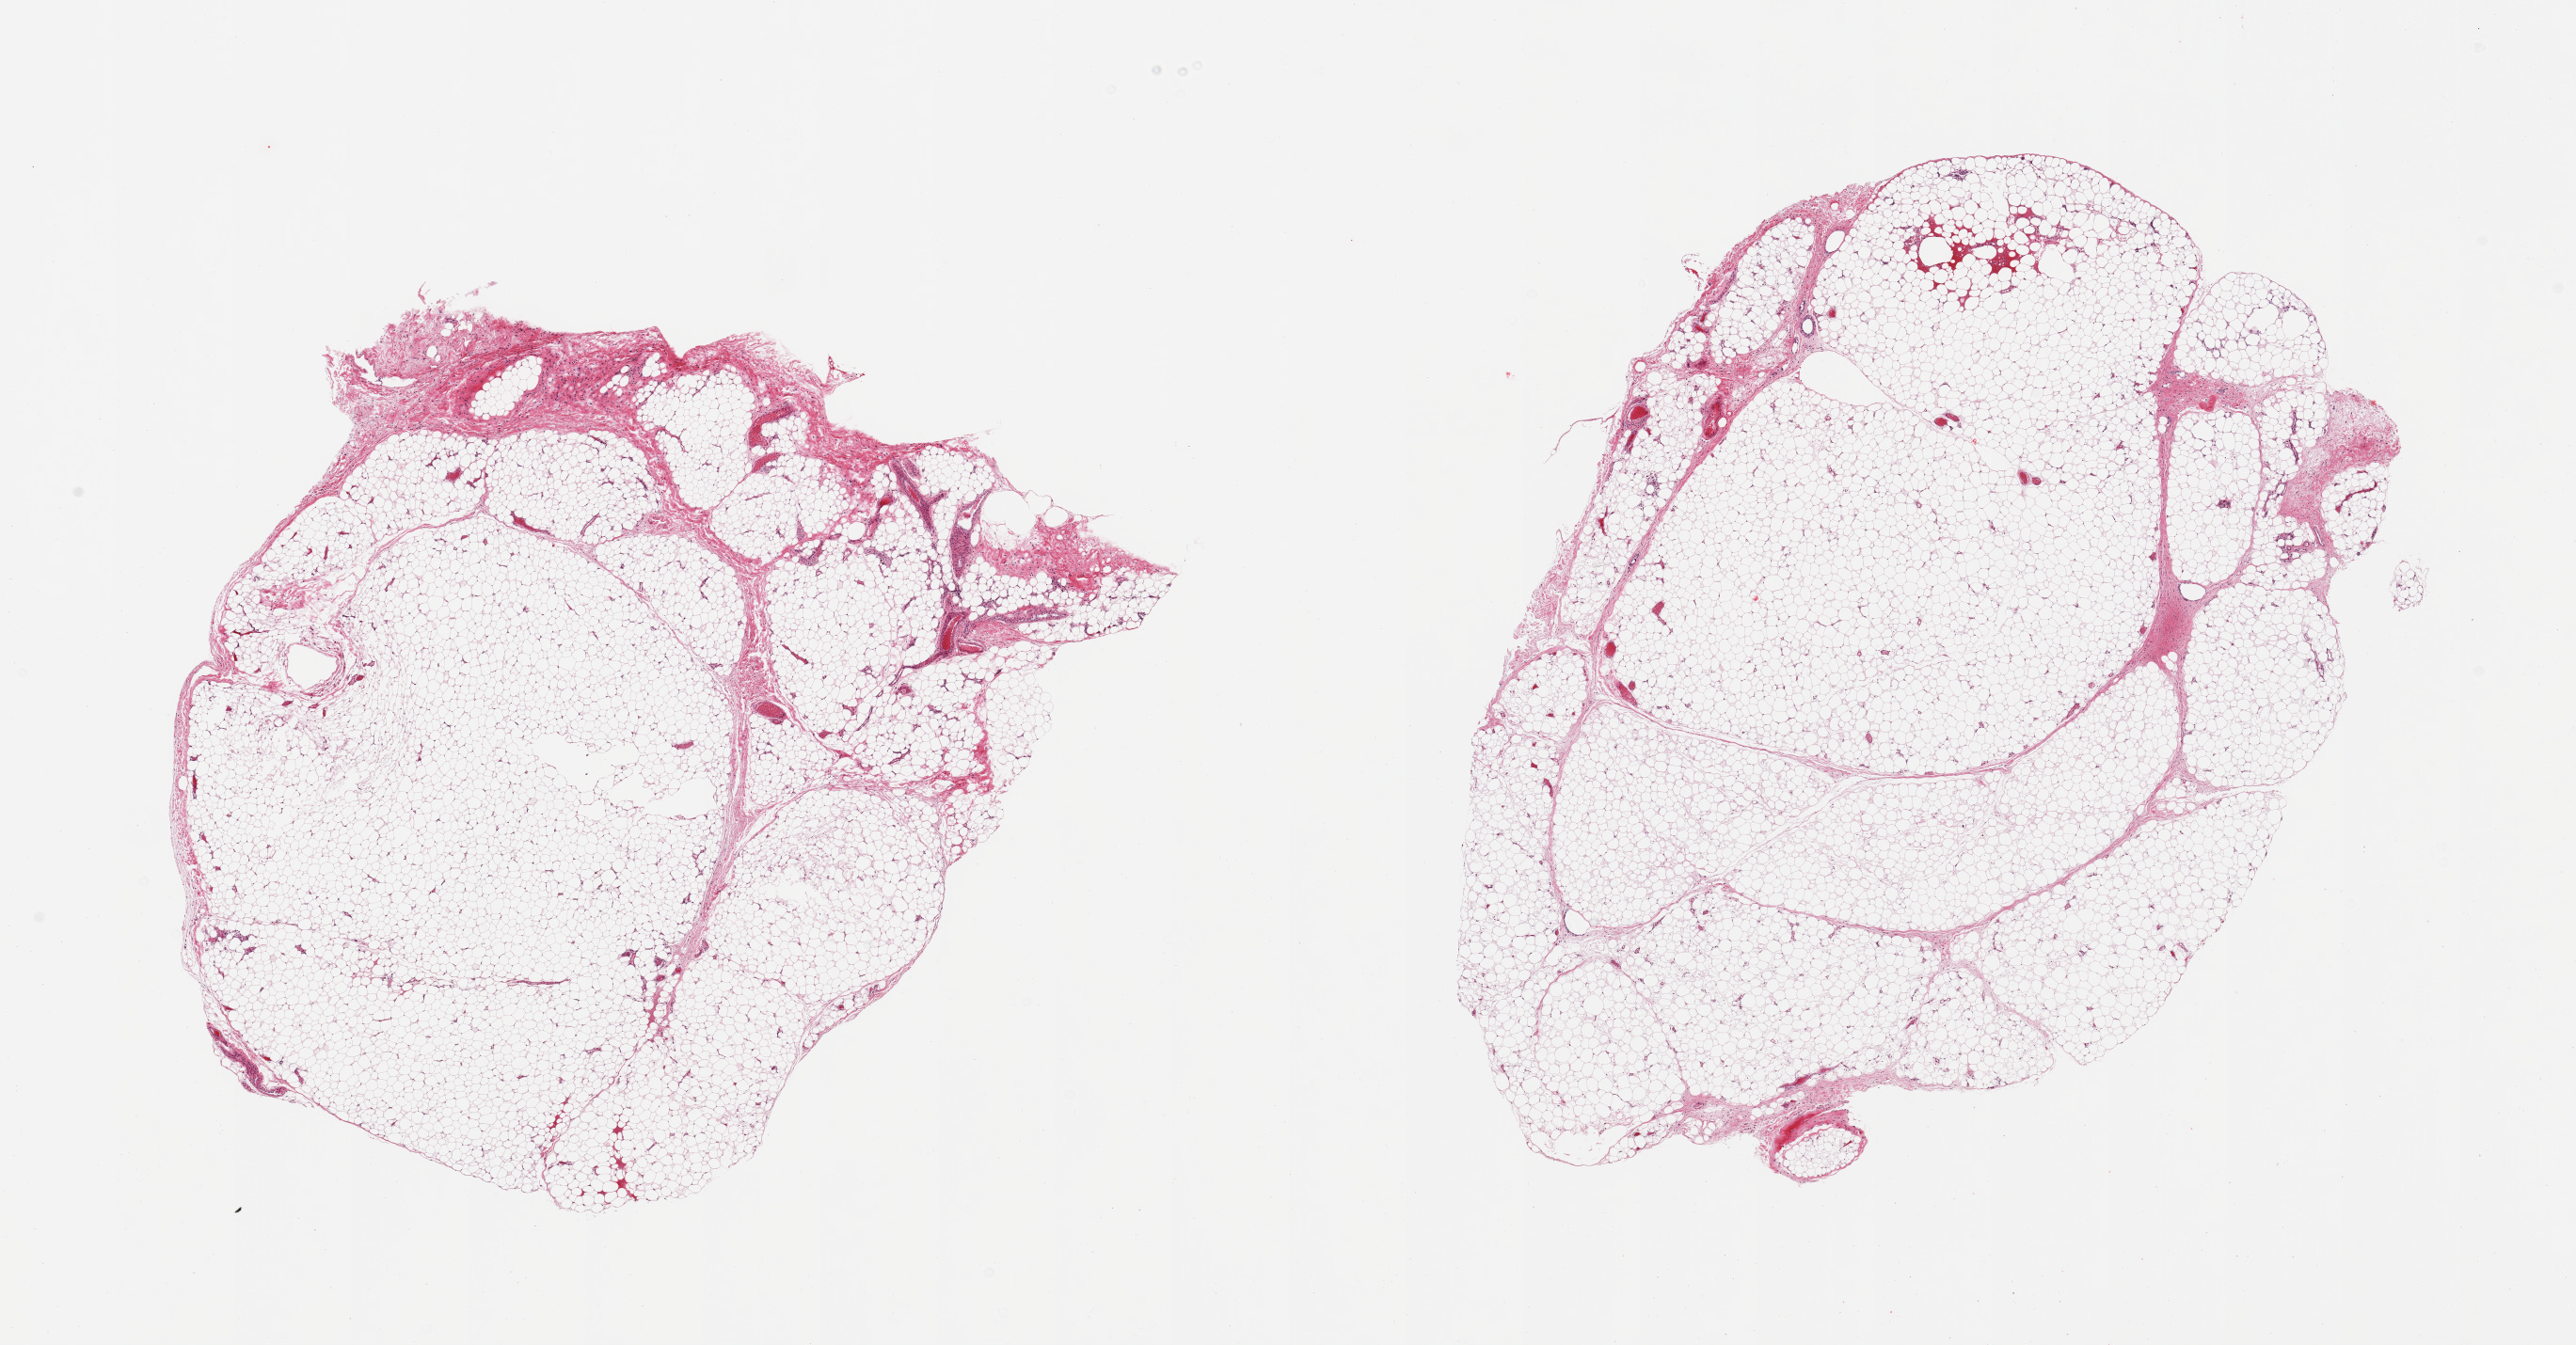
Whole-slide image, haematoxylin and eosin stain, whole scanned area (about 21.7 x 11.3 mm) shown as a low-resolution overview, PAXgene-fixed, paraffin-embedded tissue, target tissue: adipose tissue, donor tissue sample. Donor sex: male.
• review note (as recorded): 2 pieces, !0-15% fascia